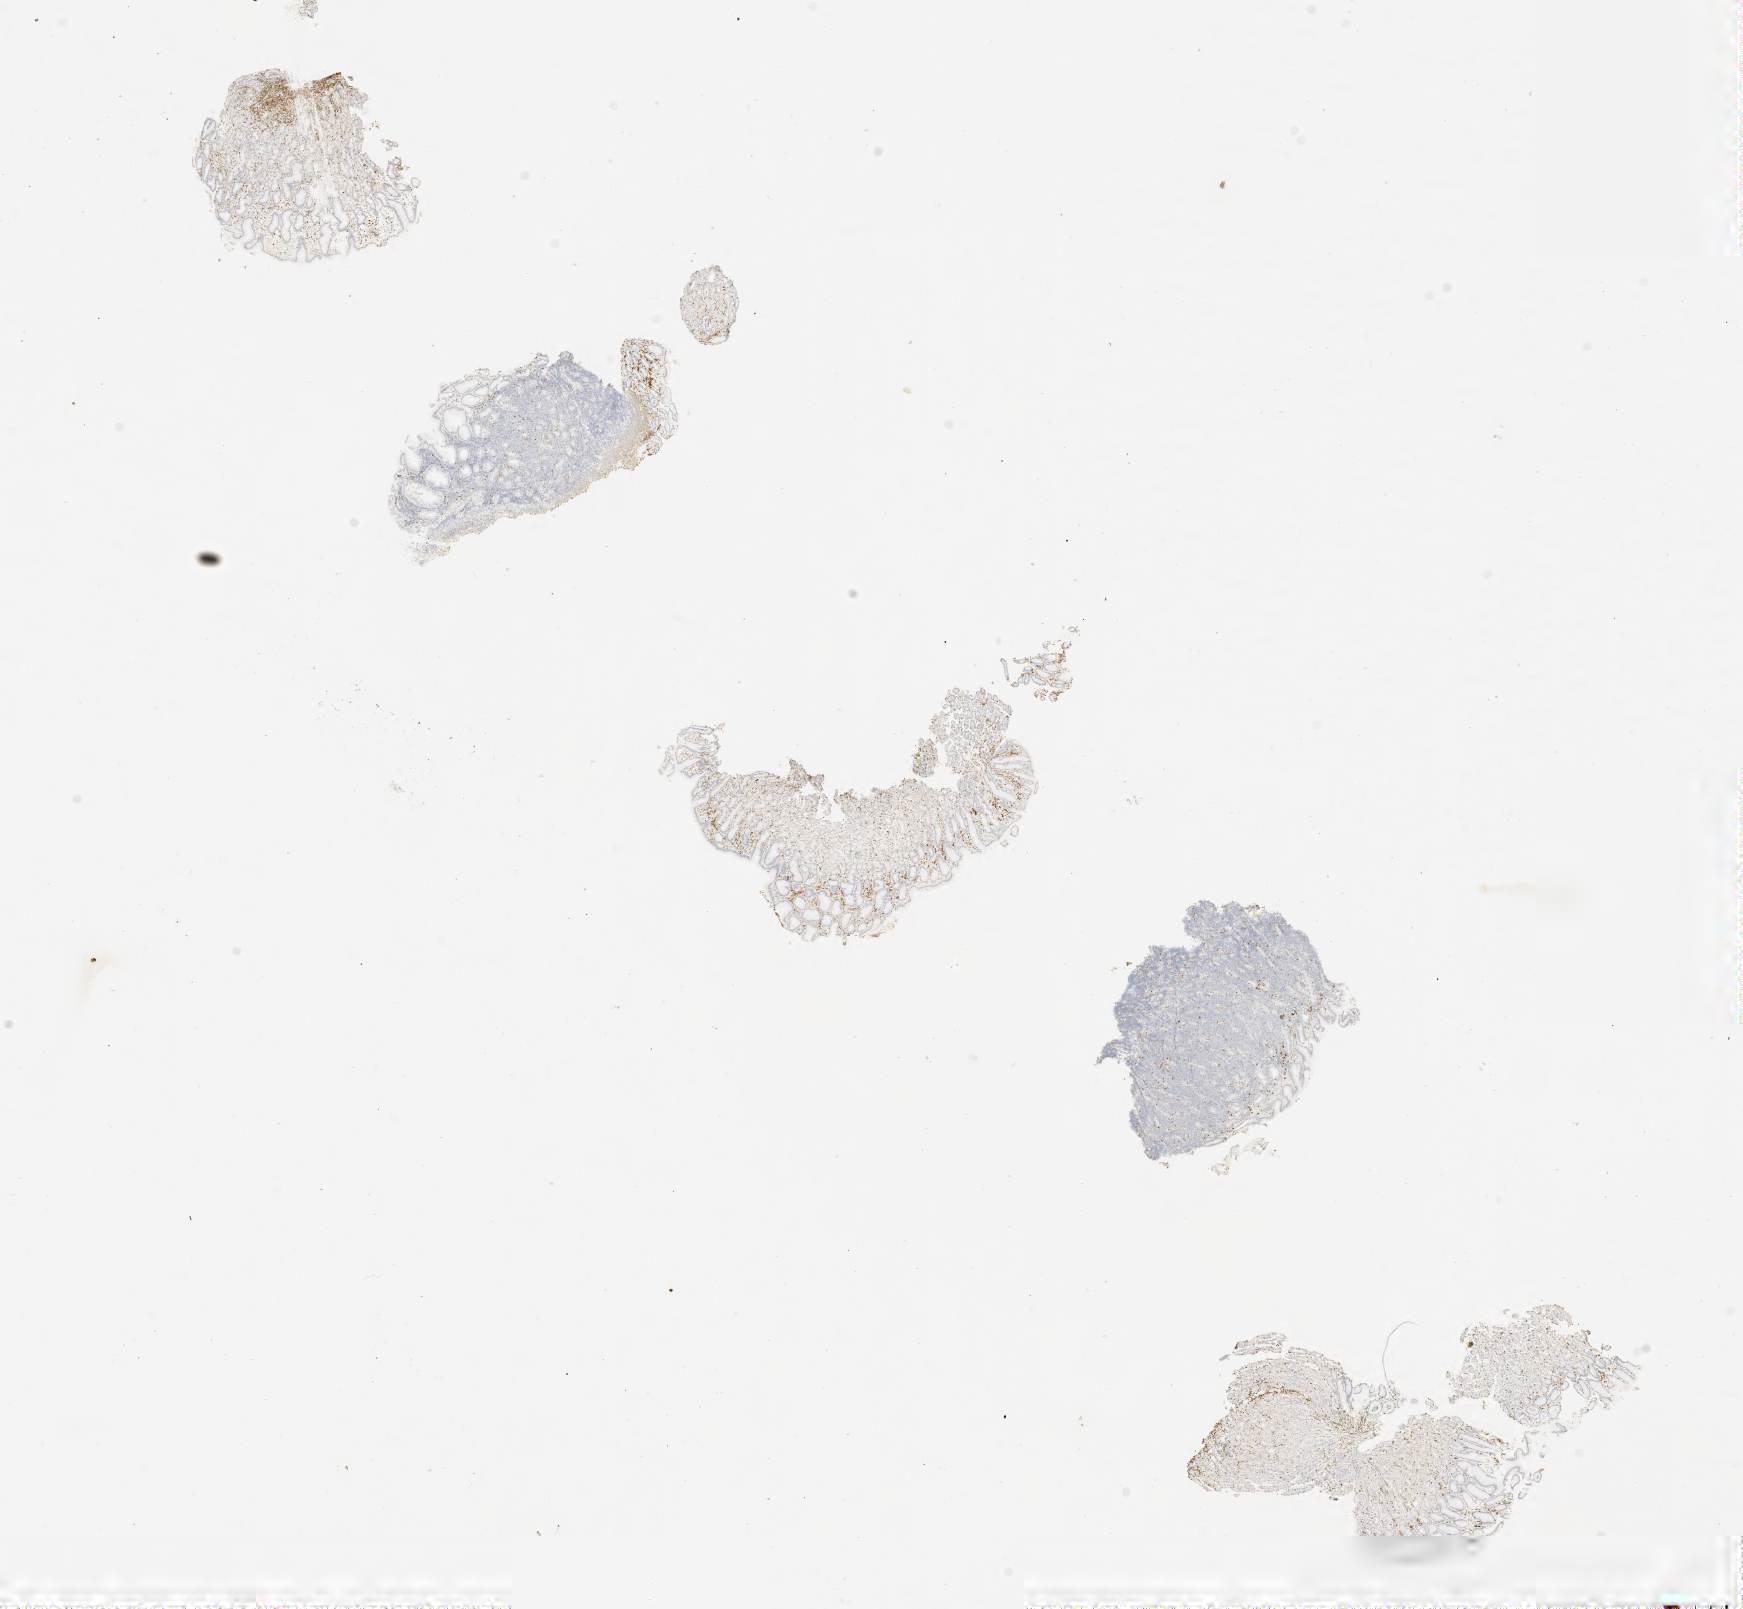
Whole-slide image, immunohistochemical stain for BCL2 — low-resolution overview of the scanned area, about 14.0 x 12.9 mm, tumor tissue. Patient male; age 40 years.
Histologic diagnosis: Burkitt lymphoma, NOS.